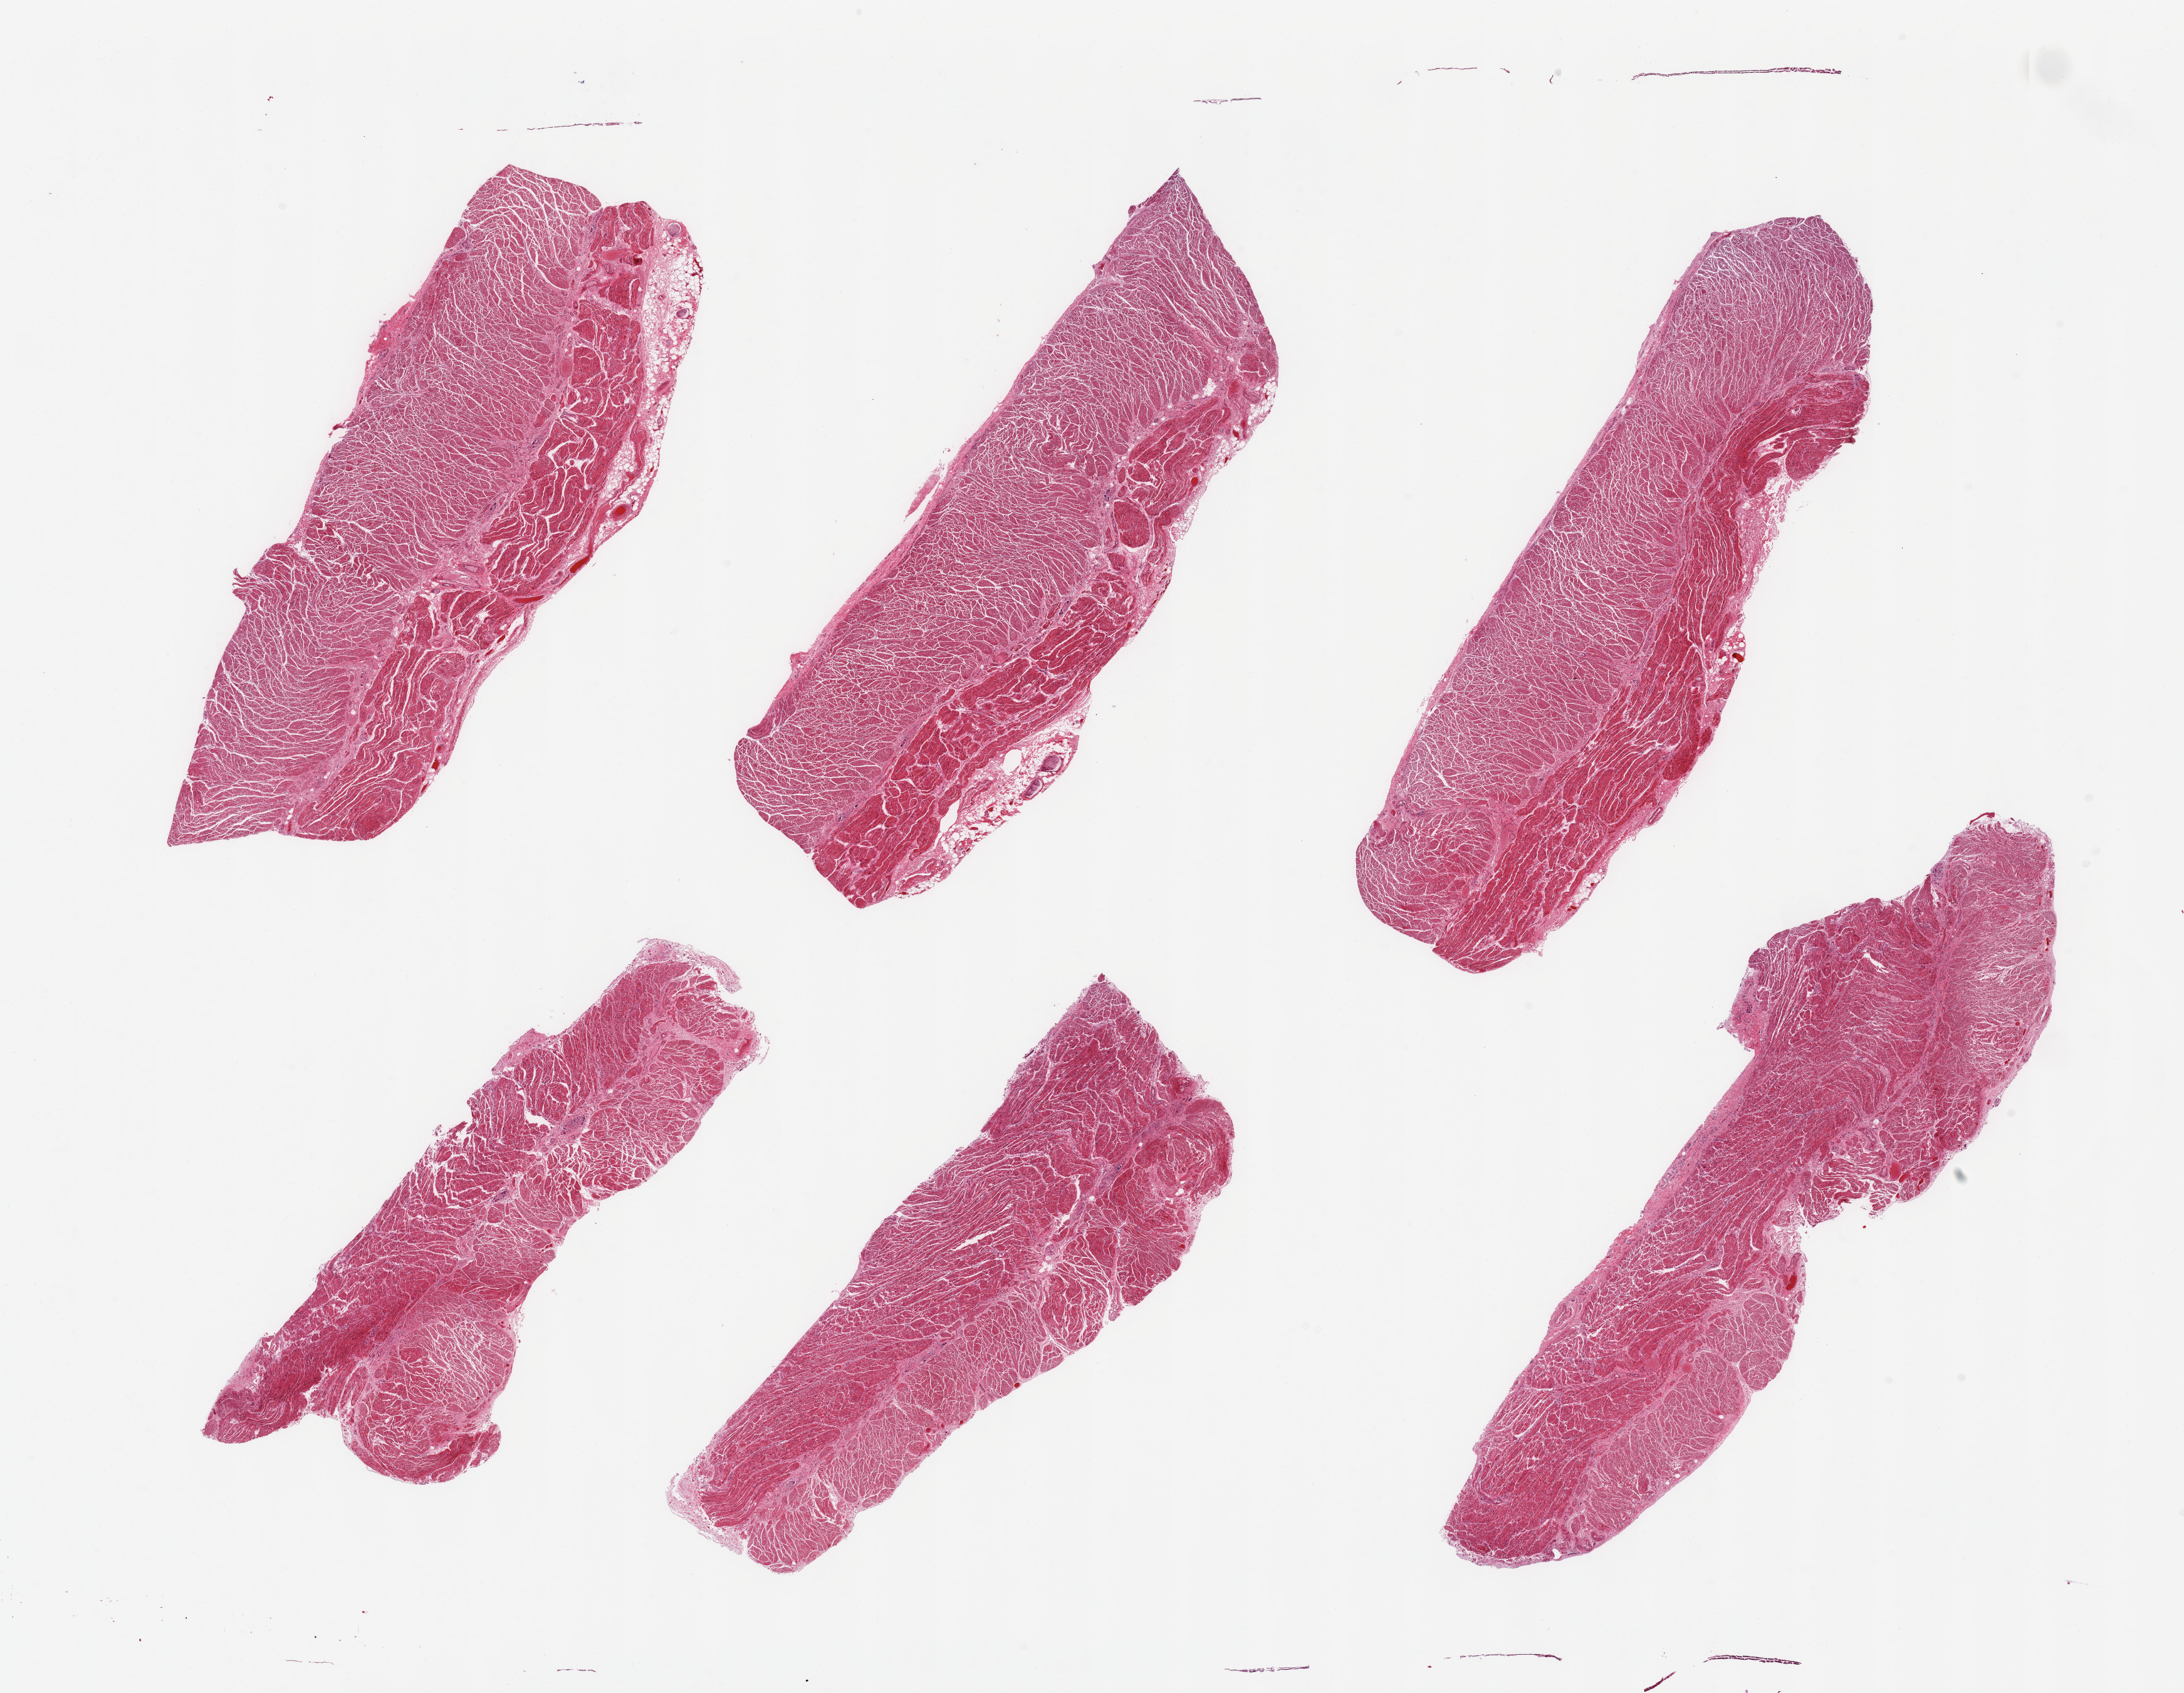
Digitized H&E-stained section, brightfield — a low-resolution overview of the entire scanned area, about 27.6 x 21.4 mm. PAXgene-fixed, paraffin-embedded tissue. Section of gastroesophageal junction (target tissue). Tissue donor sample. Male donor.
• reviewer comment on this tissue sample: 6 pieces; target muscularis, small portion of attached fat/nerve